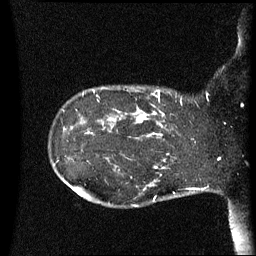
Breast MRI (dynamic contrast-enhanced), one sagittal slice. Position 15 of 60 along the scan axis. Dynamic contrast-enhanced series, image 2 of 3 at this slice position (ordered by acquisition). 1.5 T. TE 4.2 ms, TR 8.4 ms. 2.5 mm slice thickness. 256 × 256 image matrix, field of view 220 × 220 mm. Patient: female, 41 years. Case-level facts recorded for this patient, not image findings: setting: breast cancer imaged before/during neoadjuvant chemotherapy; receptor status: HER2-positive.
Structures marked on this image (semi-automatic segmentation, software-assisted and operator-edited):
- analysis volume of interest (the breast-tissue region the enhancement analysis was run in; not a lesion): bounding box <122,86,195,137> (left, top, right, bottom; pixels)
- tumour enhancement mask (voxels above the 70 % enhancement threshold inside the analysis volume of interest): <125,92,182,137>